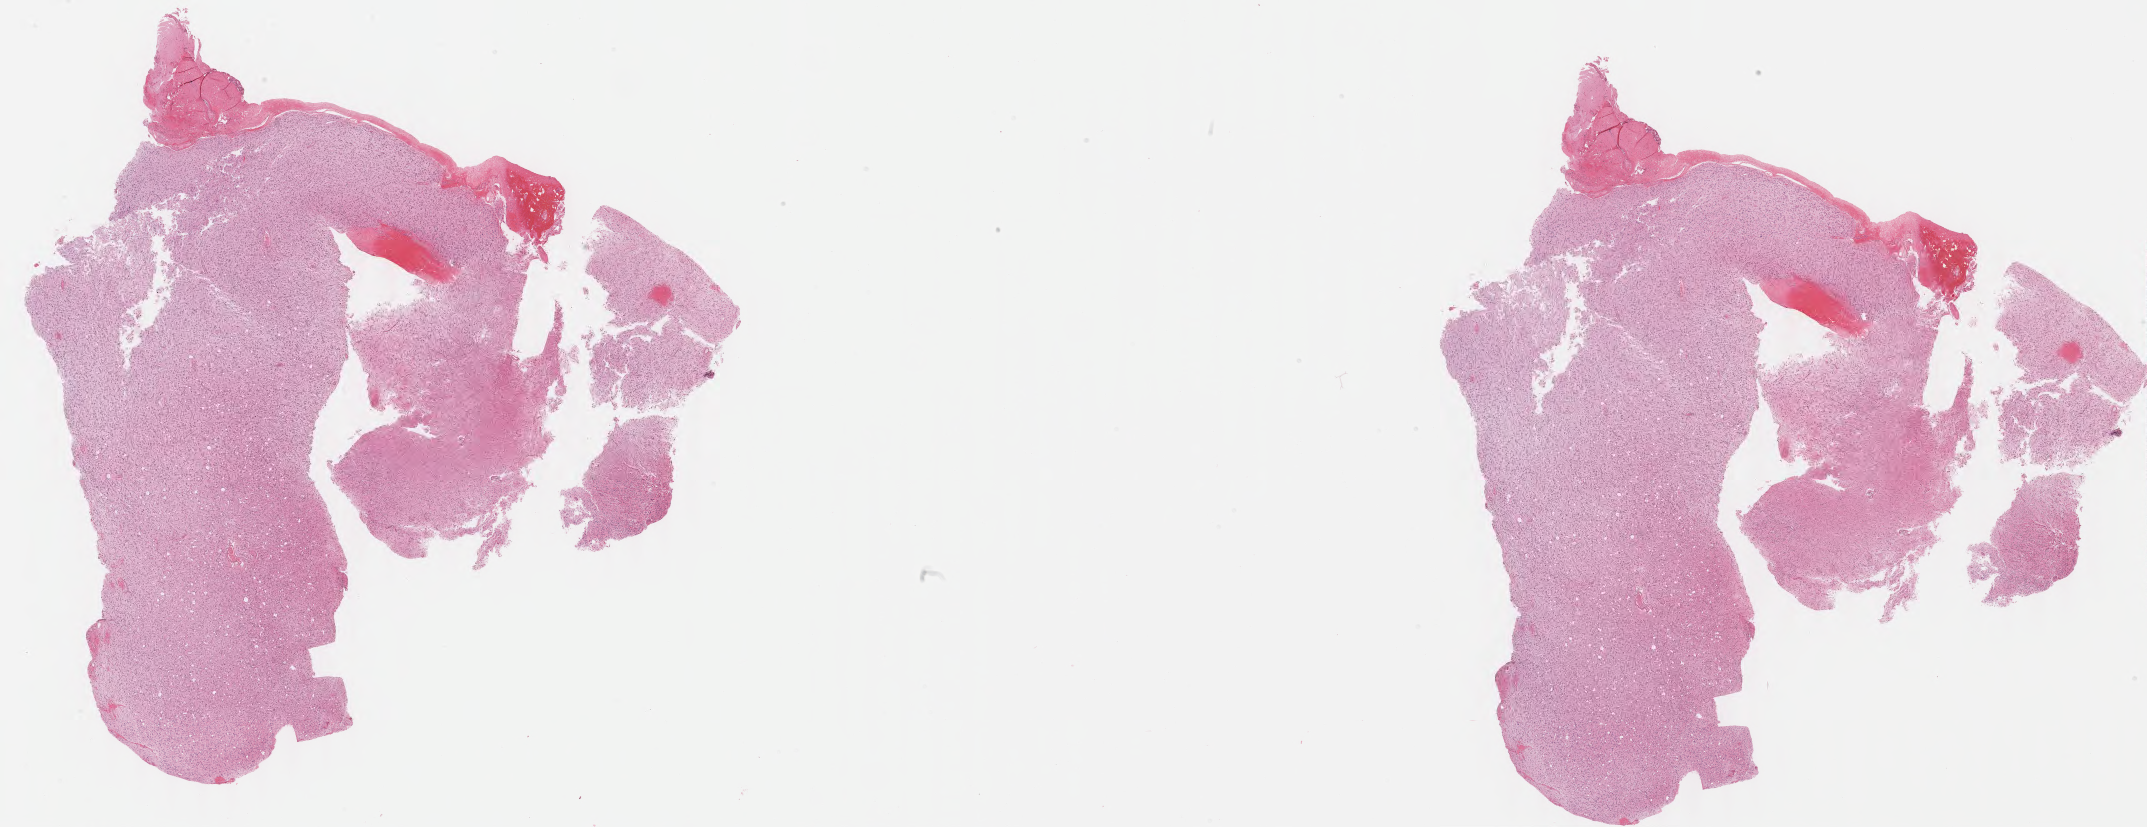
H&E-stained whole-slide image — low-resolution overview of the scanned area, about 33.9 x 13.1 mm (acquisition: 40x scan), formalin-fixed paraffin-embedded (FFPE) diagnostic section, brain, primary tumour sample. Female patient; age at initial diagnosis 36 years. Histologic grade: G3 (poorly differentiated).
Diagnosis: Astrocytoma, anaplastic (cerebrum). Laterality: left.